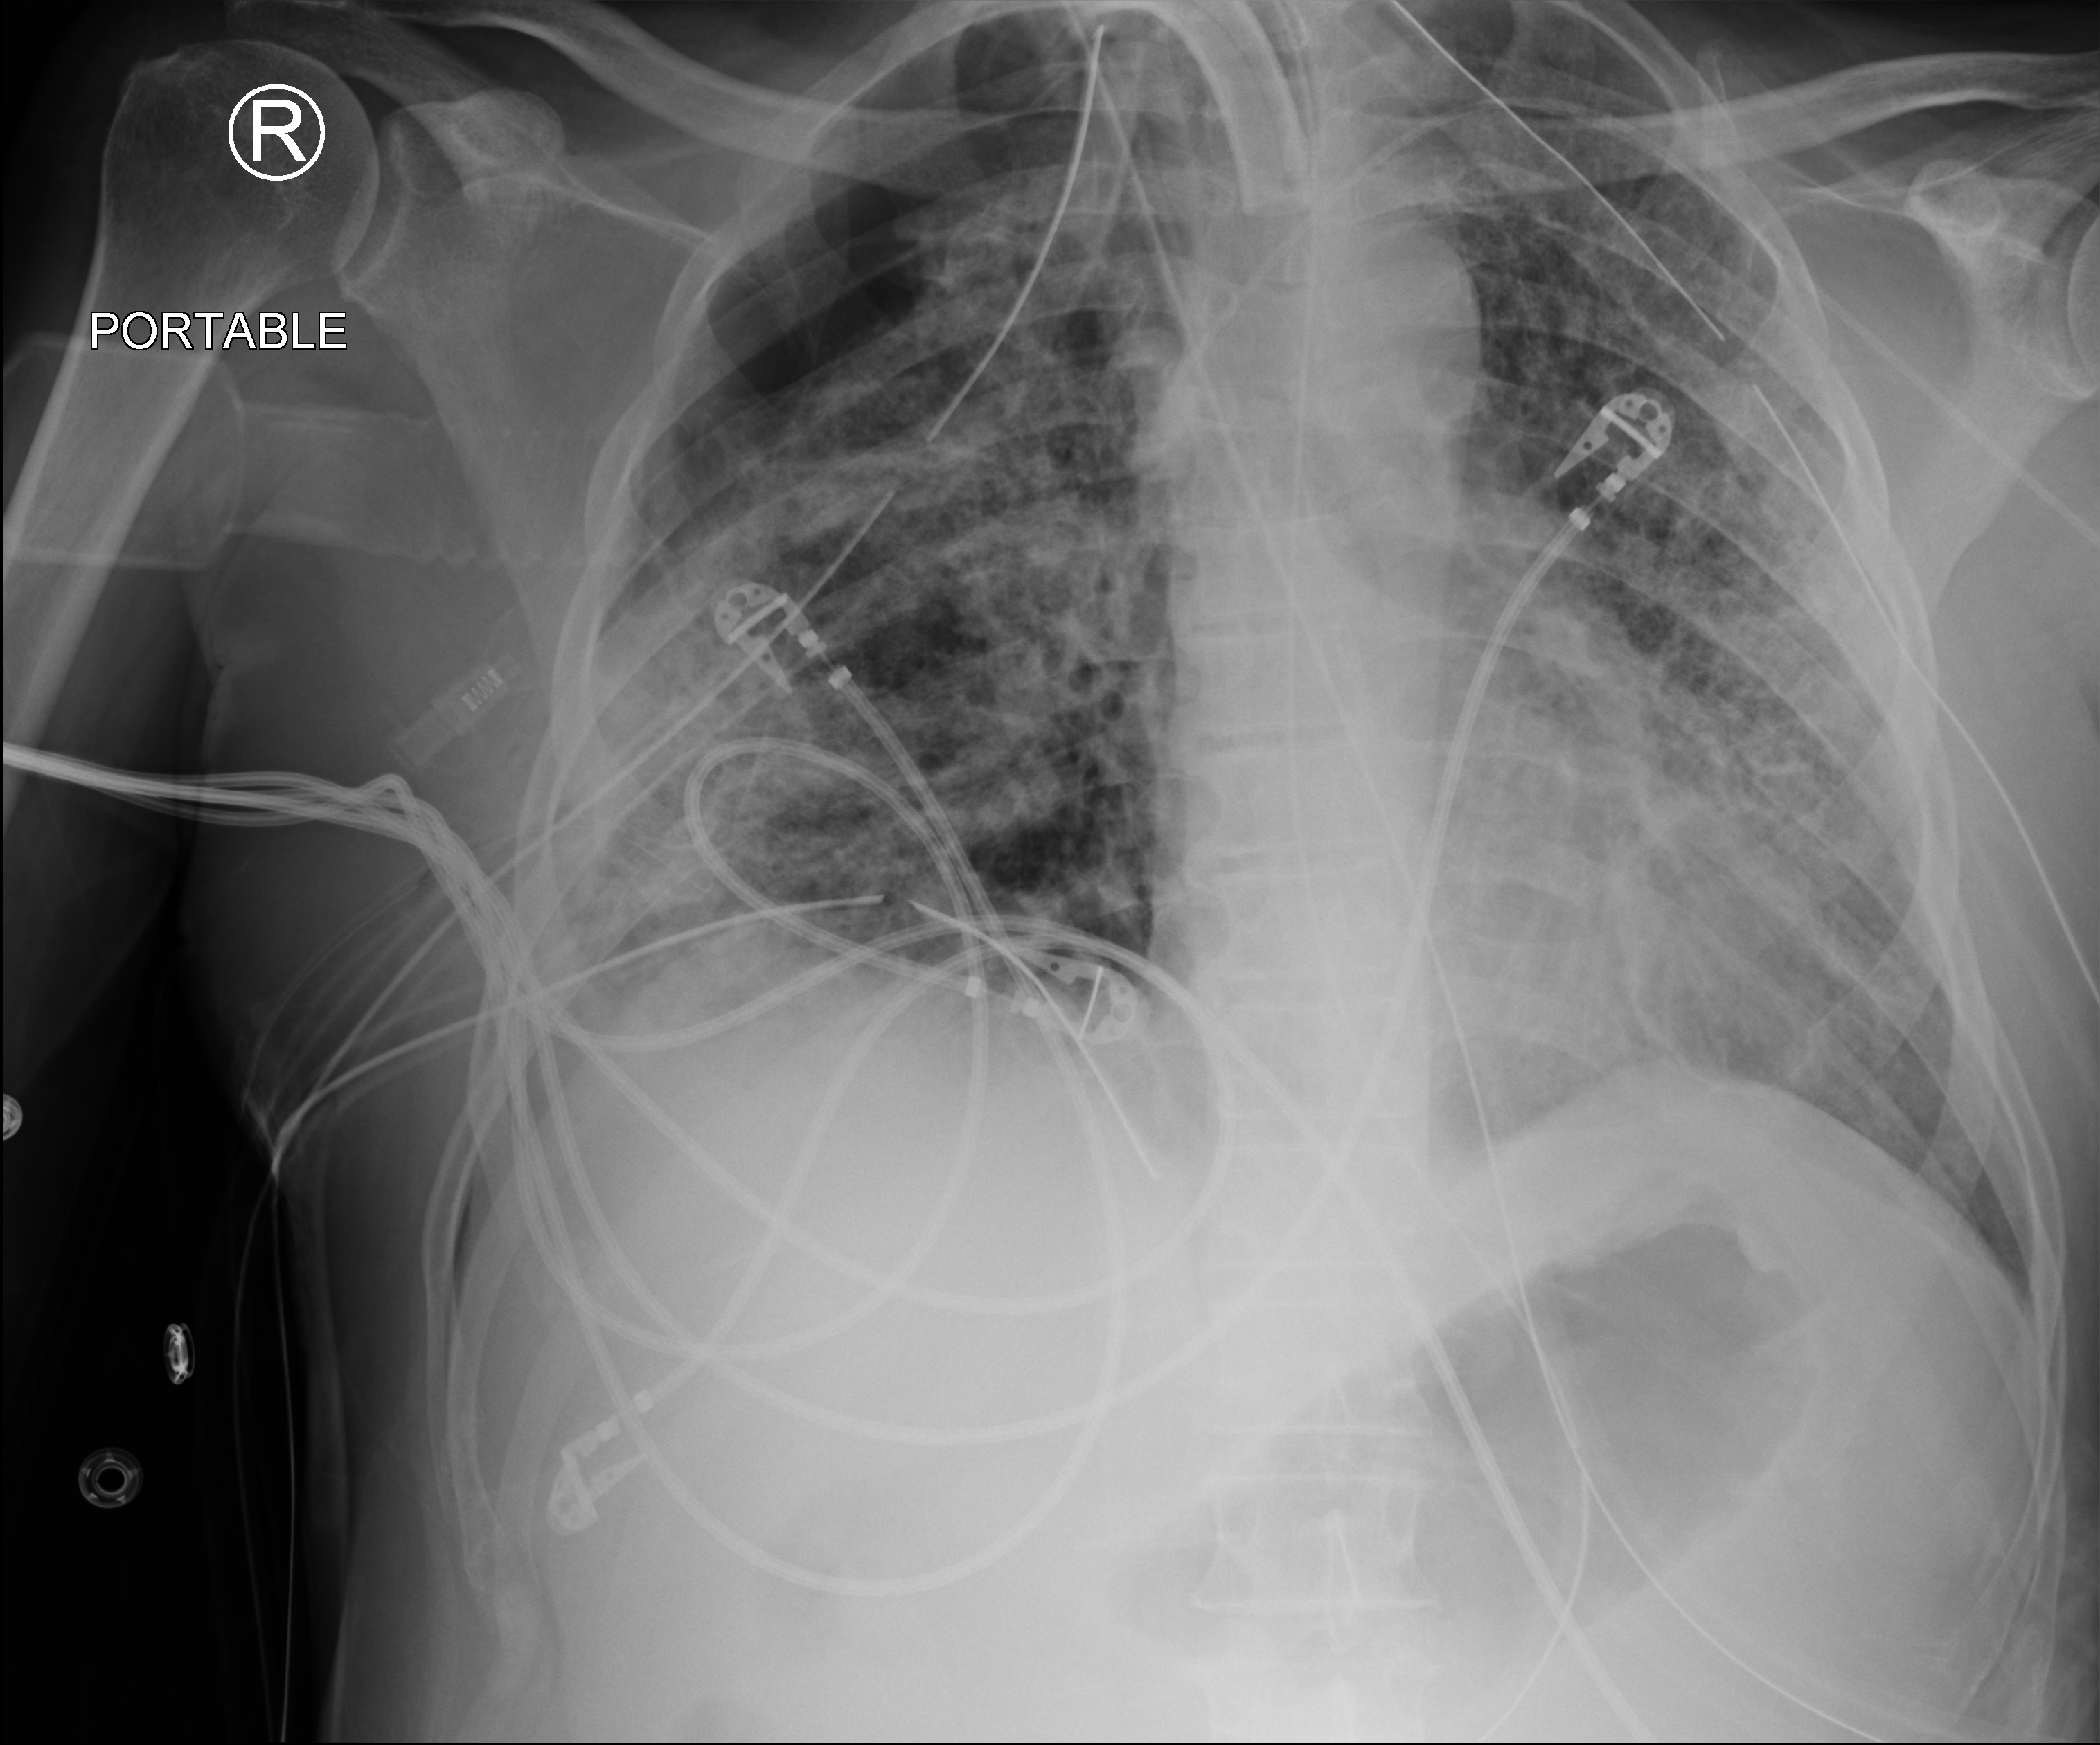
Portable chest radiograph; anteroposterior (AP) projection. Male patient hospitalised with COVID-19, age 18–59 years.
Hospital-stay facts (about this admission, not read from this image; timing relative to this image not recorded):
- mechanically ventilated during this hospital stay: yes
- COPD (admission record): no
- length of hospital stay: 83 days